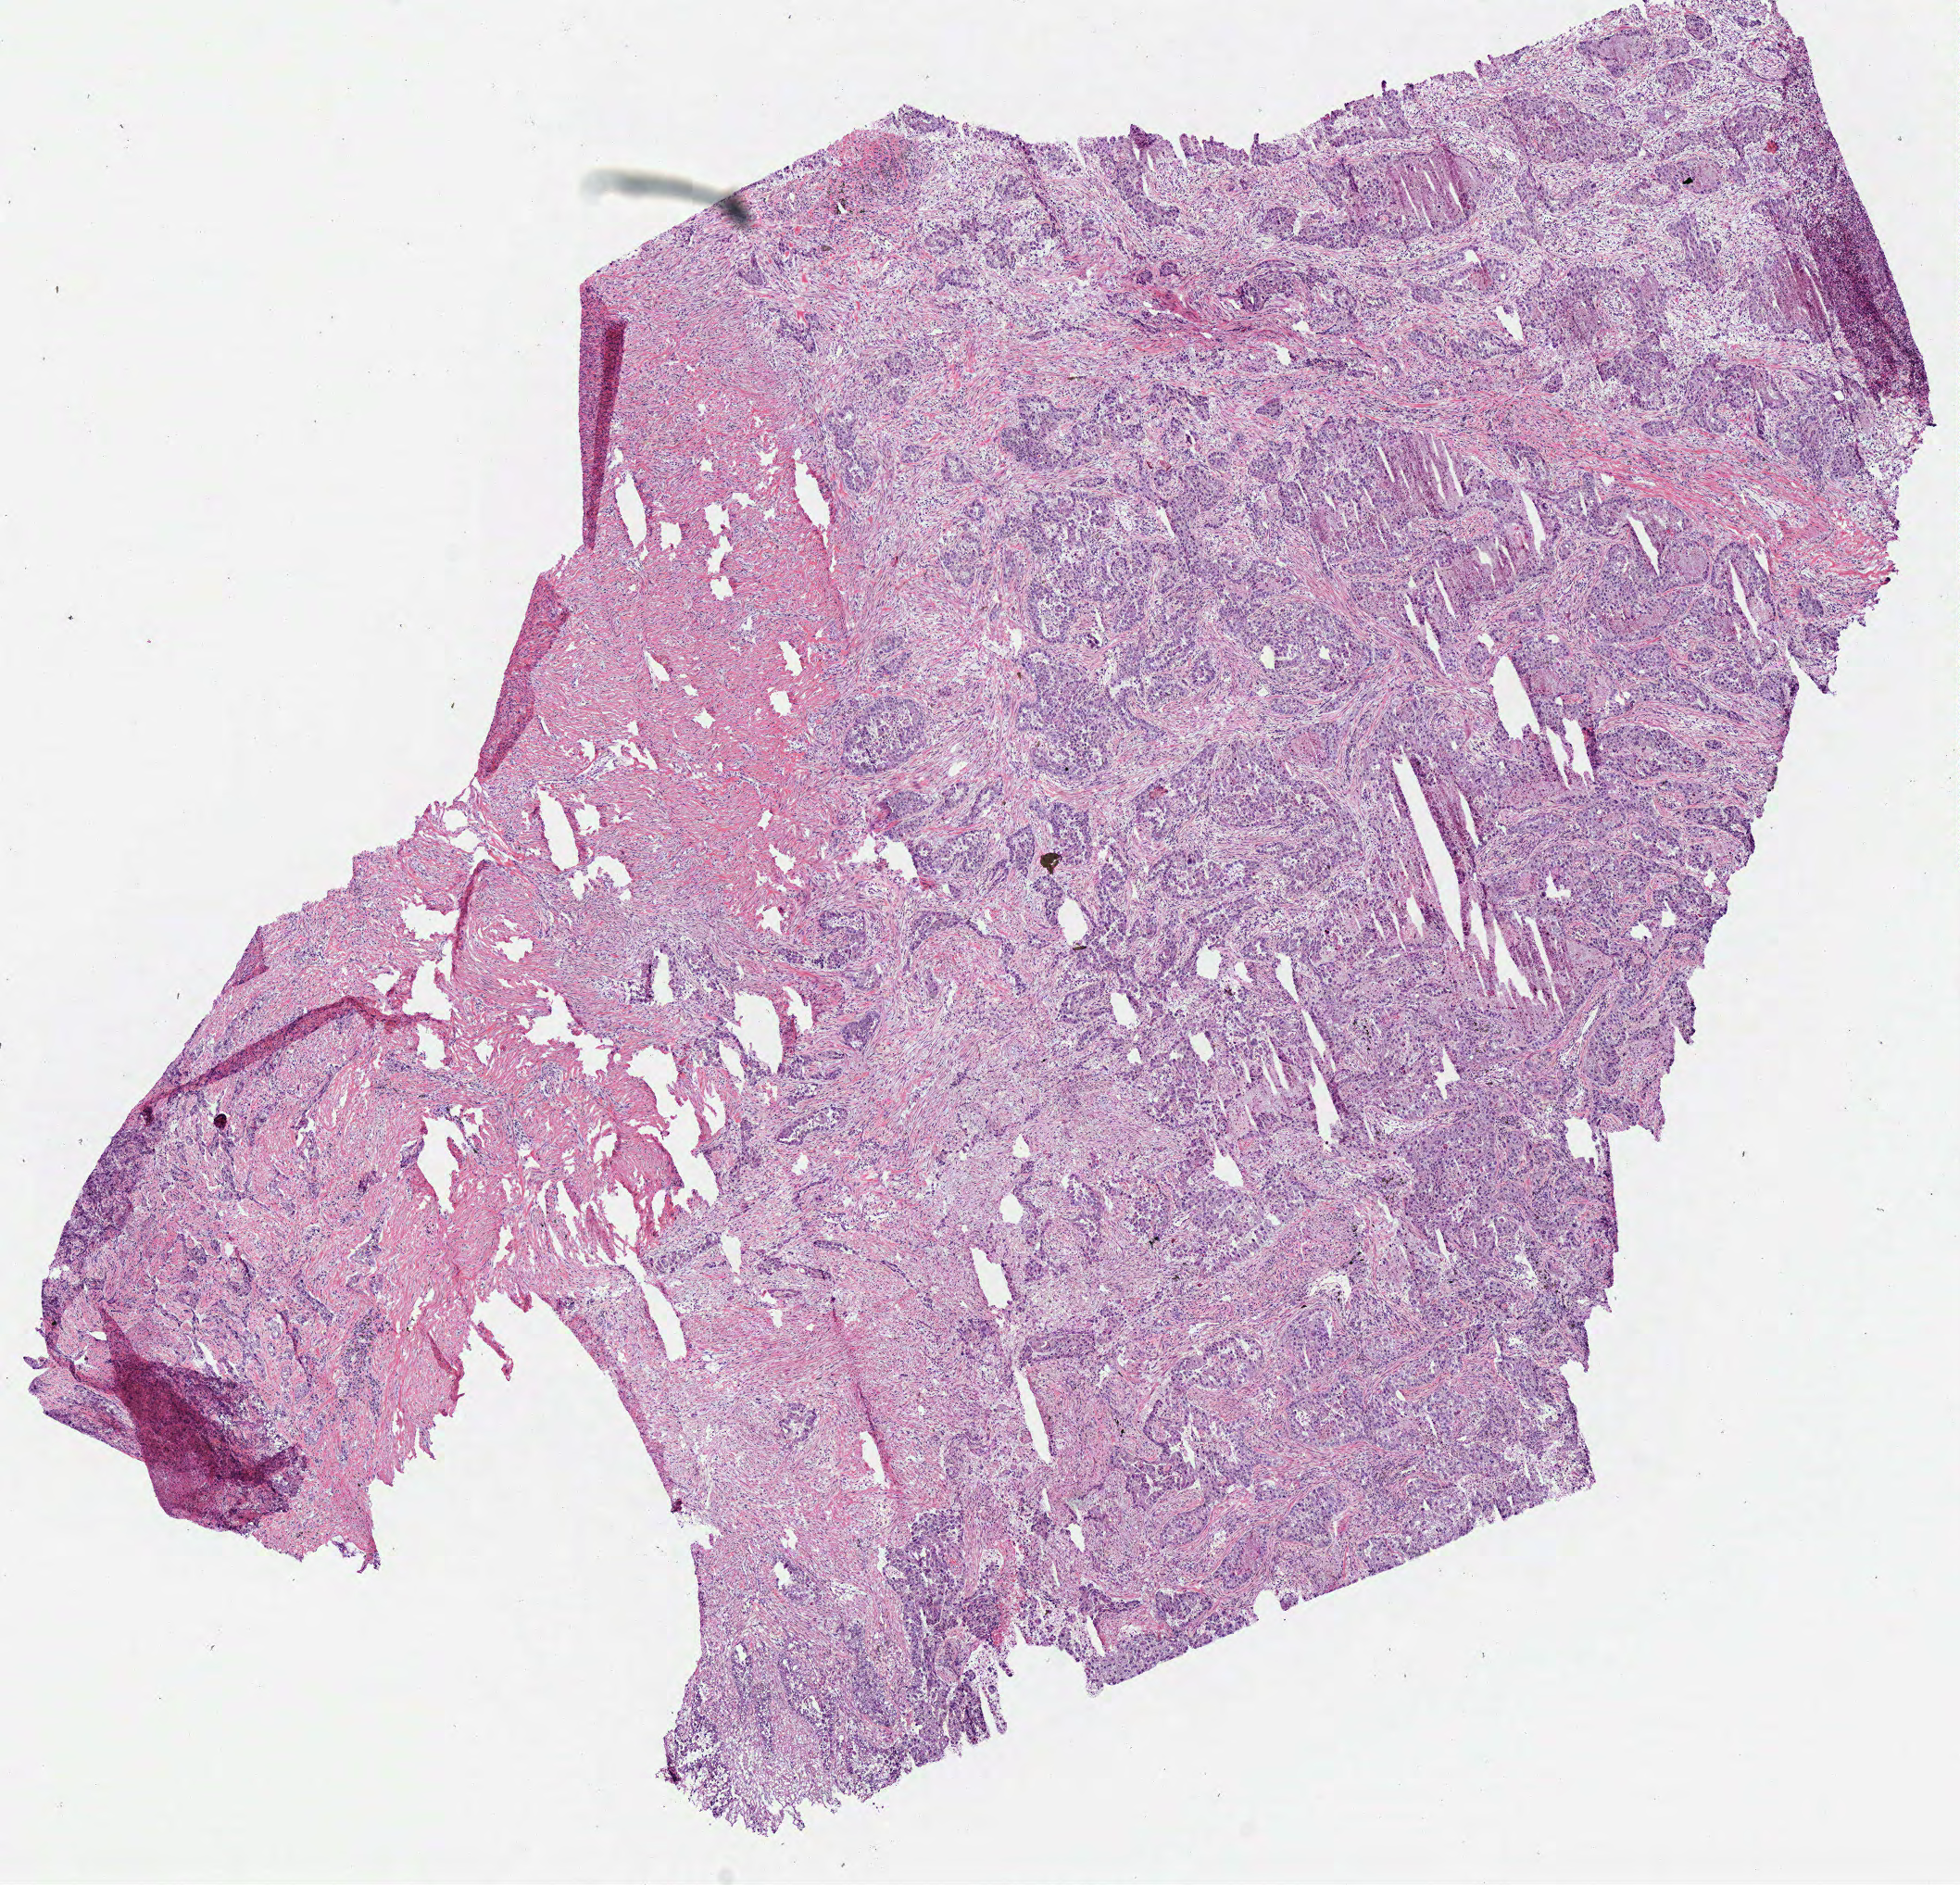
H&E whole-slide image, shown as a low-resolution overview of the whole scanned area (about 8.3 x 8.0 mm). Frozen section. Primary tumour sample from the lung. Patient: female, age at initial diagnosis 56 years. Composition of this section per pathologist review: tumour cells 80%, tumour nuclei 61%, normal cells 0%, stromal cells 10%, necrosis 10%. Infiltration values recorded for this section: lymphocyte infiltration 10%, monocyte infiltration 2%, neutrophil infiltration 10%.
- laterality: left
- AJCC pathologic stage: IIIA (7th edition)
- pathologic diagnosis: Adenocarcinoma, NOS (lower lobe, lung)